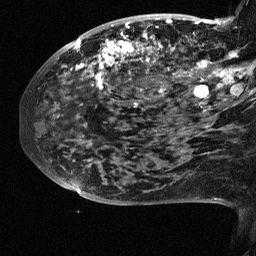
Breast MRI (dynamic contrast-enhanced), one sagittal slice; slice 23 of 64 in the series (ordered by position); dynamic contrast-enhanced study with each time point stored as its own series, time point 2 of 3 at this slice position (early post-contrast, ordered by acquisition time); 1.5 T; TE 4.5 ms, TR 11 ms; 256 × 256 image matrix, field of view 200 × 200 mm. Patient: female, 38 years. From the clinical record (not read from this slice): setting: breast cancer imaged before/during neoadjuvant chemotherapy; receptor status: HR-positive, HER2-negative.
Annotated regions visible in this slice (semi-automatically segmented with operator editing):
- analysis volume of interest (the breast-tissue region the enhancement analysis was run in; not a lesion): bounding box (x1, y1, x2, y2) in pixels: (88, 18, 252, 126)
- tumour enhancement mask (voxels above the 90 % enhancement threshold inside the analysis volume of interest): (92, 19, 252, 111)